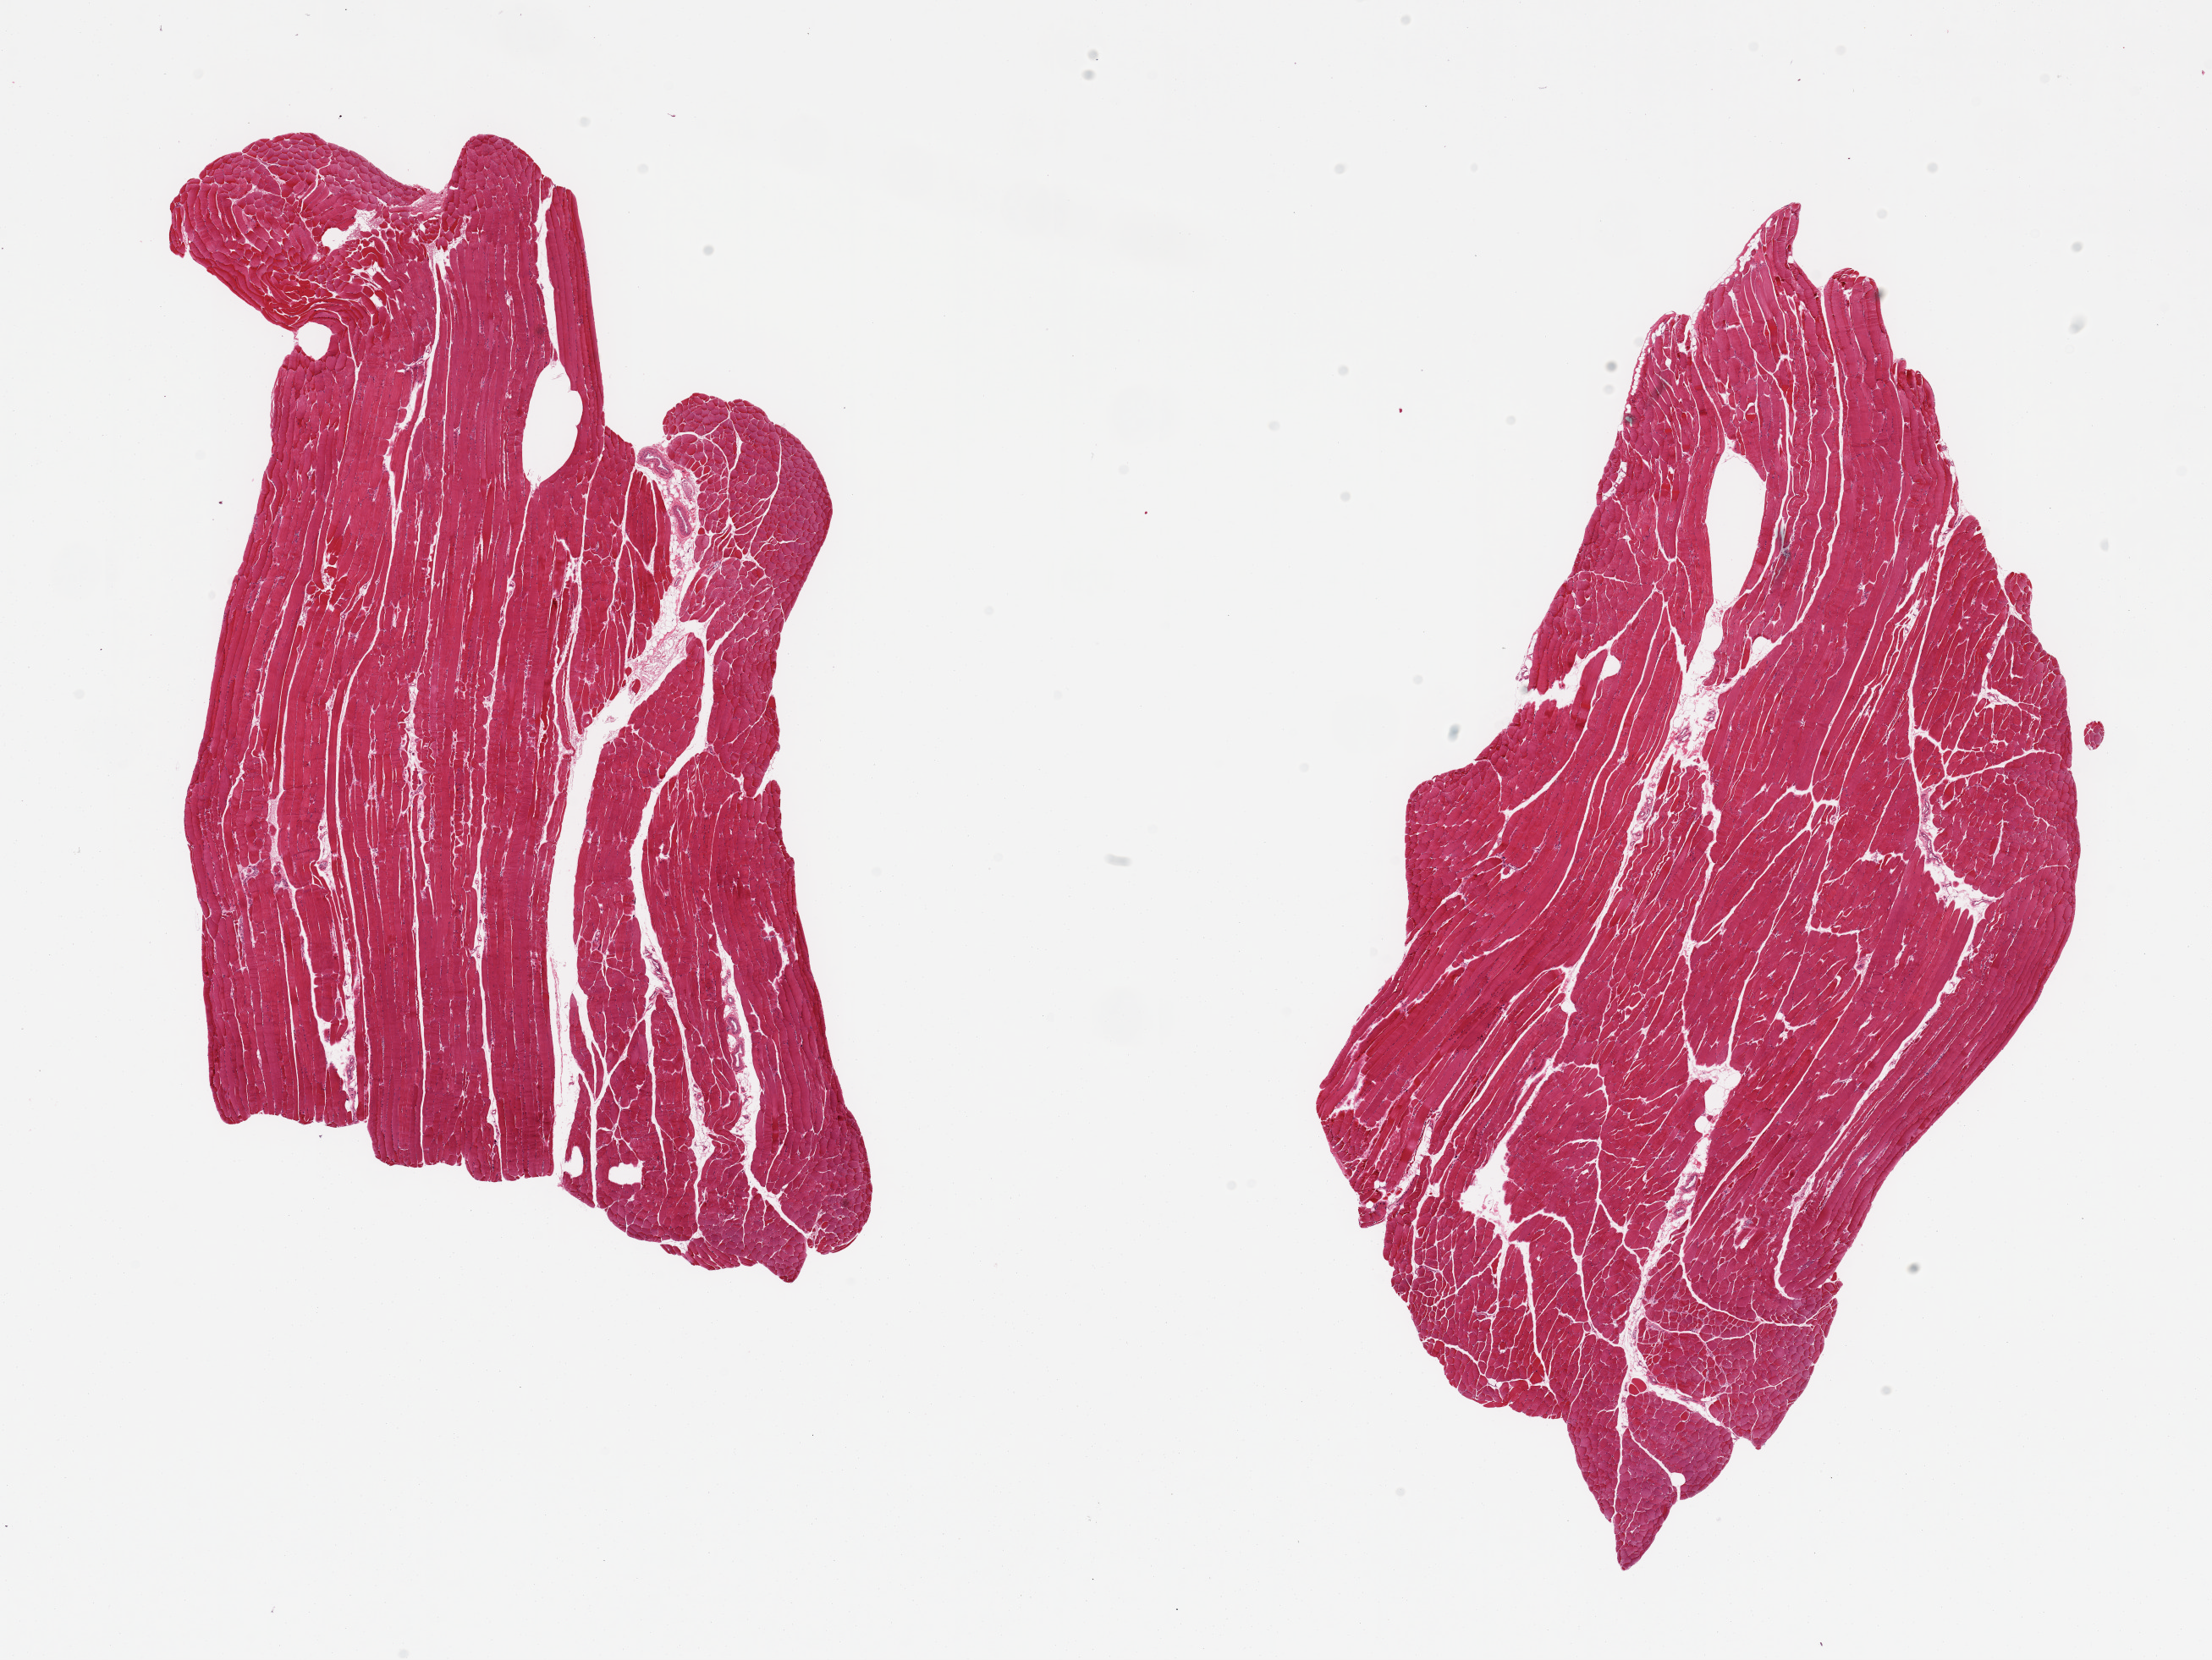
Hematoxylin and eosin (H&E) whole-slide image, brightfield — shown as a low-resolution overview of the whole scanned area (about 20.7 x 15.5 mm); PAXgene-fixed, paraffin-embedded tissue; sampled site (target tissue): skeletal muscle; tissue donor sample. Donor sex: female.
Pathologist's review note for this sample: 2 pieces ~10% interstitial fat/vascular tissue.